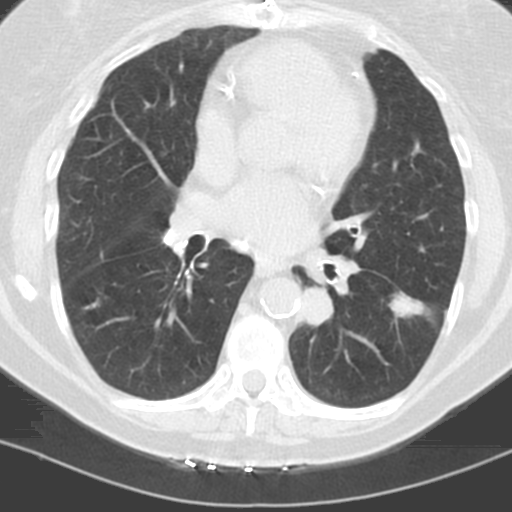
Low-dose screening chest CT, axial slice. Baseline screening round. Lung window (W 1500 / L -600 HU). Slice 67 of 121 in the series. Female participant, aged 60 years at enrolment.
- 2 lesions marked by an expert reader on this slice (largest first), bounding box (x1, y1, x2, y2) in pixels: (291, 281, 340, 333); (373, 286, 428, 332).
- The screening reader recorded 3 non-calcified nodules or masses ≥4 mm on this exam (left lower lobe, left lower lobe, right middle lobe); which of them these boxes mark is not recorded.
- Official screen result: positive, change unspecified: nodule(s) >= 4 mm or enlarging nodule(s), mass(es), or other non-specific abnormalities suspicious for lung cancer.
- Later outcome: lung cancer diagnosed 96 days after this screen — adenocarcinoma, NOS, left lower lobe, stage IV (AJCC 6th edition), 22 mm at pathology.